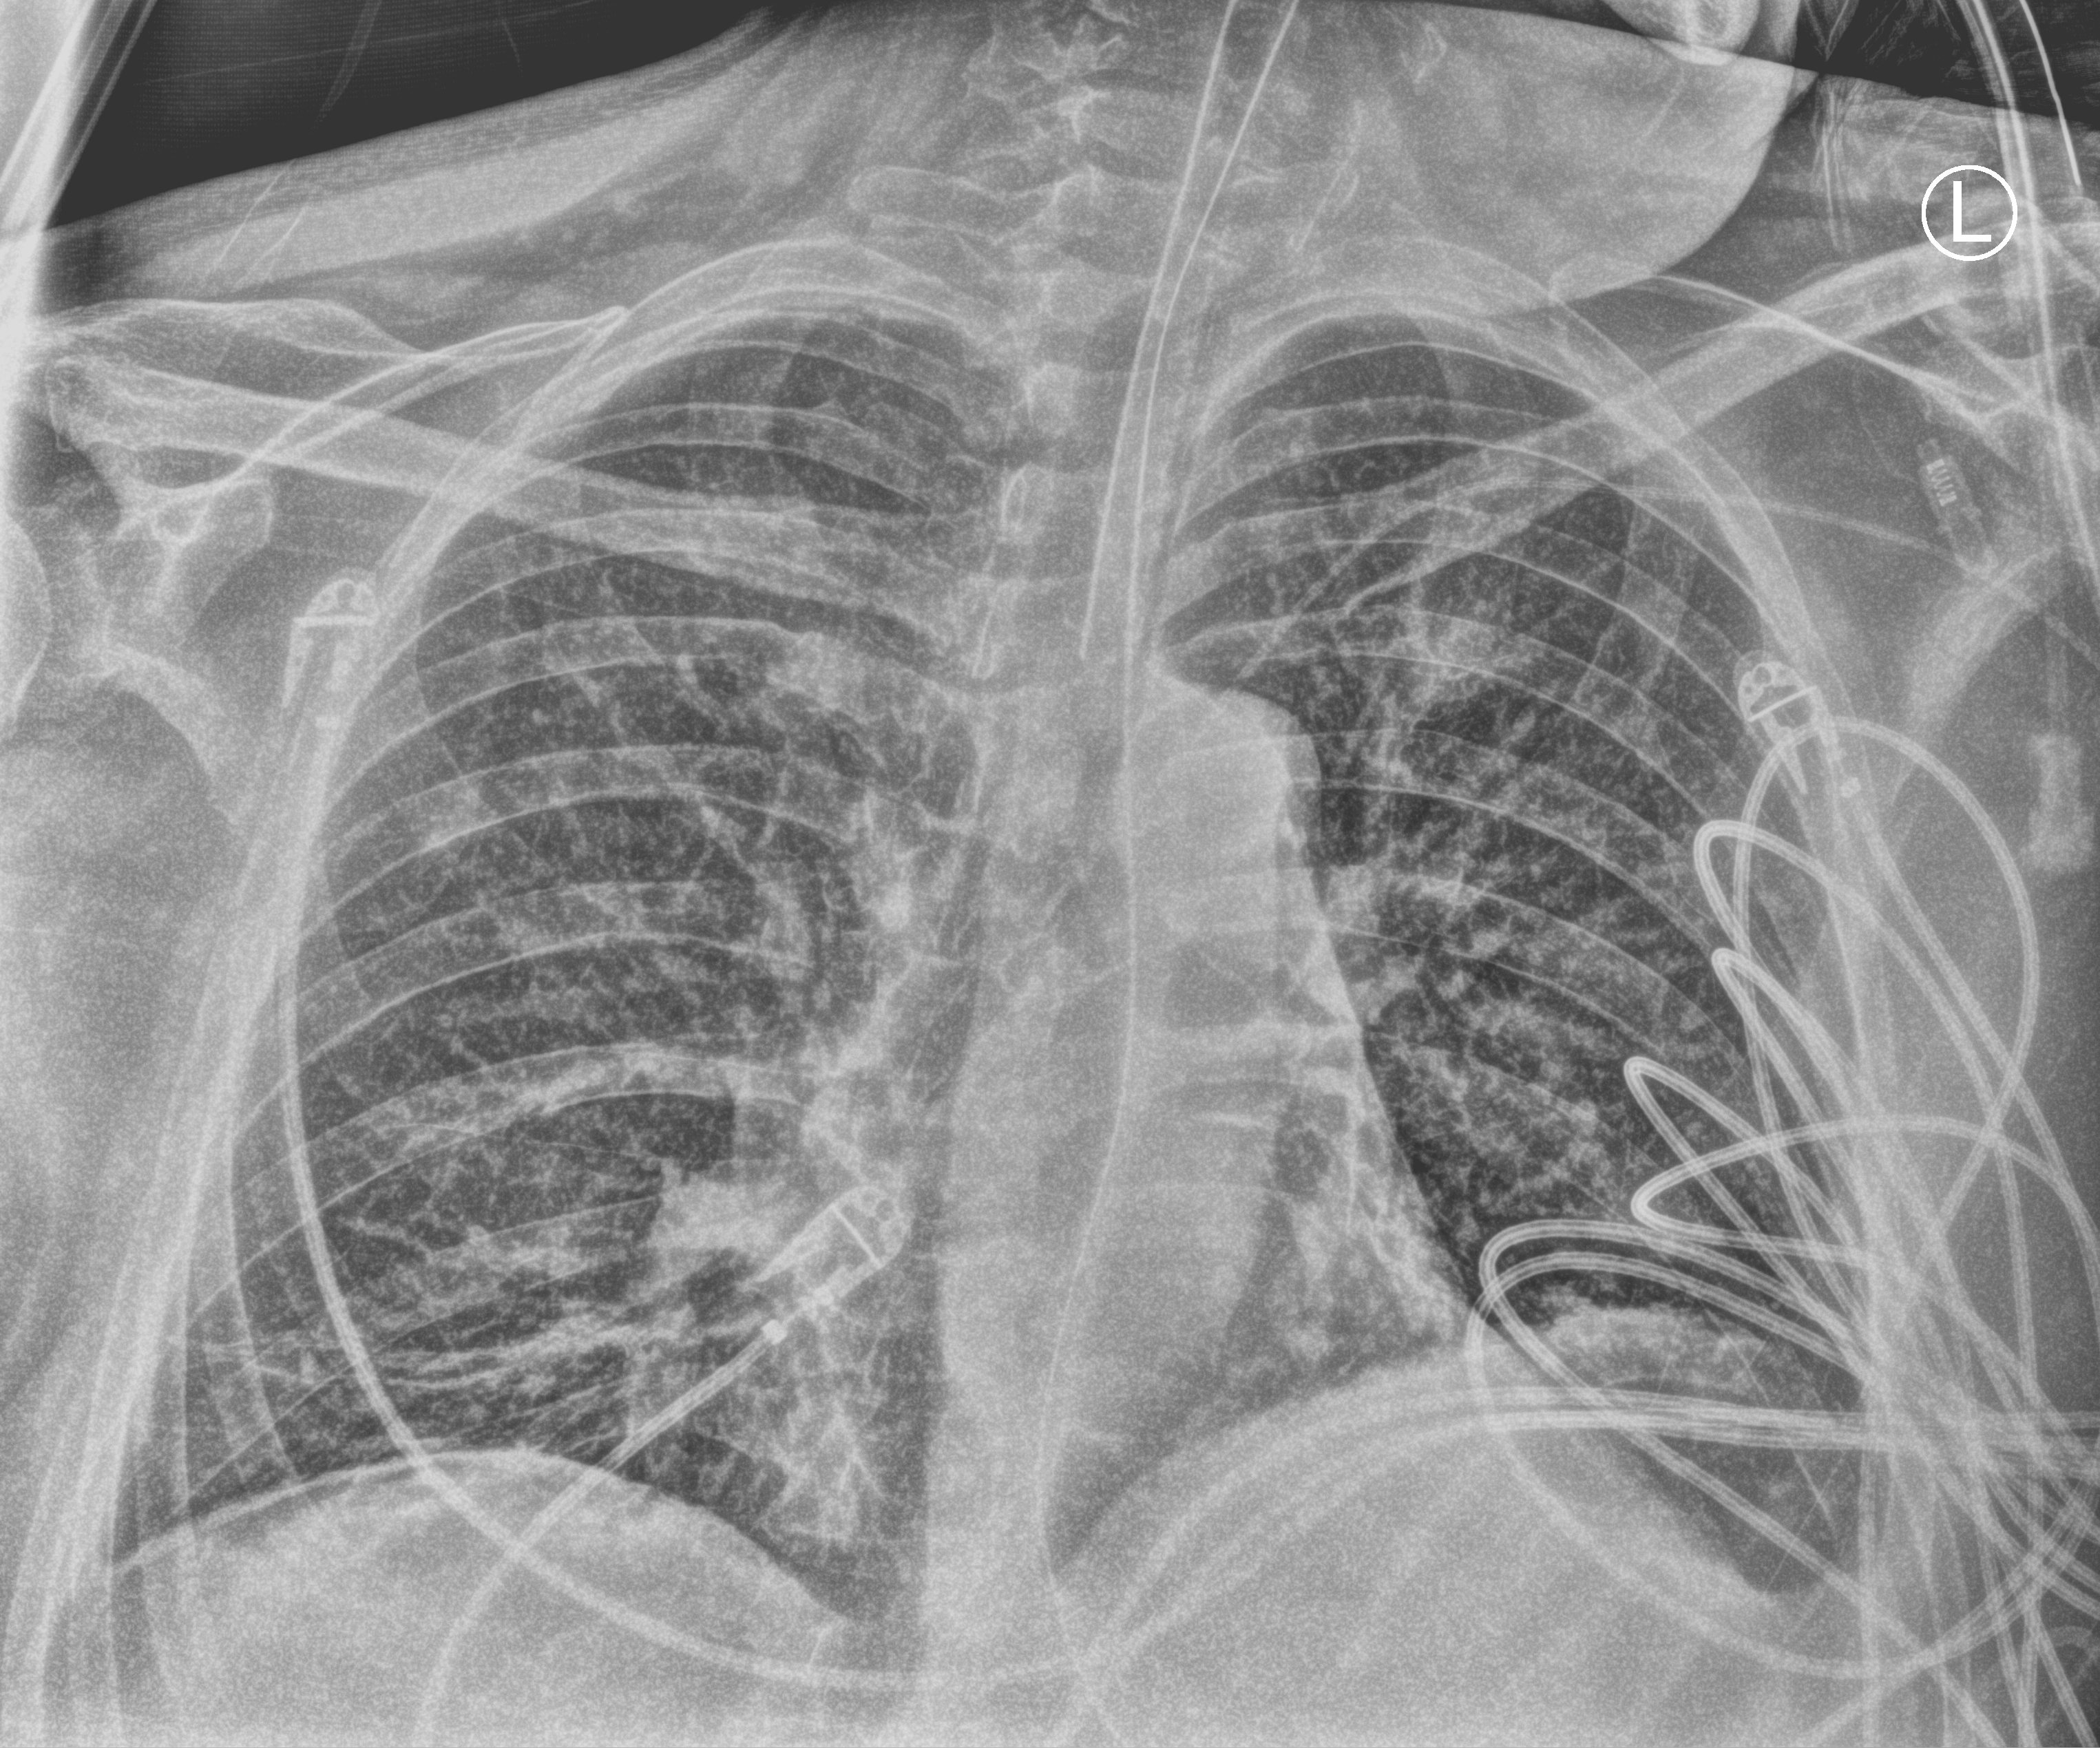
Portable chest radiograph, anteroposterior (AP) projection. Patient hospitalised with COVID-19; male, aged 60–74 years.
From the hospital-stay record, not from the radiograph (when in the stay this image was taken is not recorded):
- mechanically ventilated during this hospital stay: yes
- admitted to intensive care during this hospital stay: yes
- hypertension (admission record): no